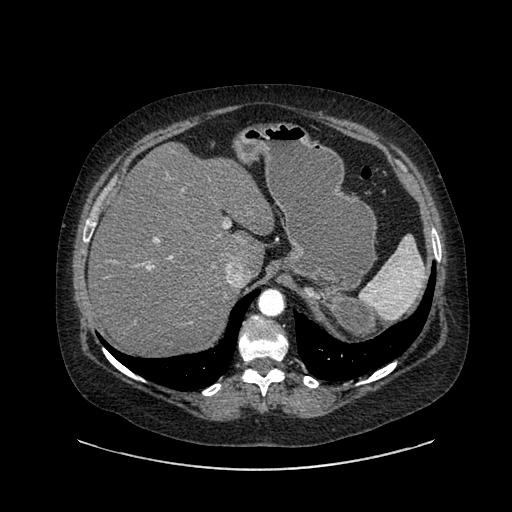
Contrast-enhanced abdominal CT, one axial slice; slice 636 of 769 in the series (ordered by position); 120 kVp; intravenous contrast given; soft-tissue window (W 400 / L 40 HU); 0.62 mm slice thickness; 512 × 512 image matrix, field of view 460 × 460 mm. Female patient, age 61 years. Case-level facts recorded for this patient, not image findings: diagnosis: adrenocortical carcinoma; tumour side: left adrenal; tumour size at pathology: 13 cm; Ki-67 index: 79 %; stage (as recorded): 2.
Outlined on this slice (semi-automatic segmentation, software-assisted and operator-edited):
- mass: bounding box [x1, y1, x2, y2] px = [309, 286, 377, 339]